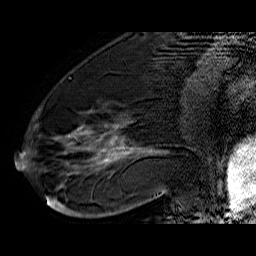
Breast MRI (dynamic contrast-enhanced), one sagittal slice; position 22 of 60 along the scan axis; dynamic contrast-enhanced series, time point 2 of 6 at this slice position (early post-contrast); 1.5 T; TE 6.4 ms, TR 32.9 ms; 4 mm slice thickness; 256 × 256 image matrix, field of view 200 × 200 mm. Female patient. Case-level facts recorded for this patient, not image findings: setting: breast cancer imaged before/during neoadjuvant chemotherapy; receptor status: HR-positive, HER2-negative.
Structures marked on this image (semi-automatically segmented with operator editing):
- analysis volume of interest (the breast-tissue region the enhancement analysis was run in; not a lesion): bounding box [x1, y1, x2, y2] px = [45, 74, 176, 210]
- tumour enhancement mask (voxels above the 100 % enhancement threshold inside the analysis volume of interest): [46, 125, 164, 208]